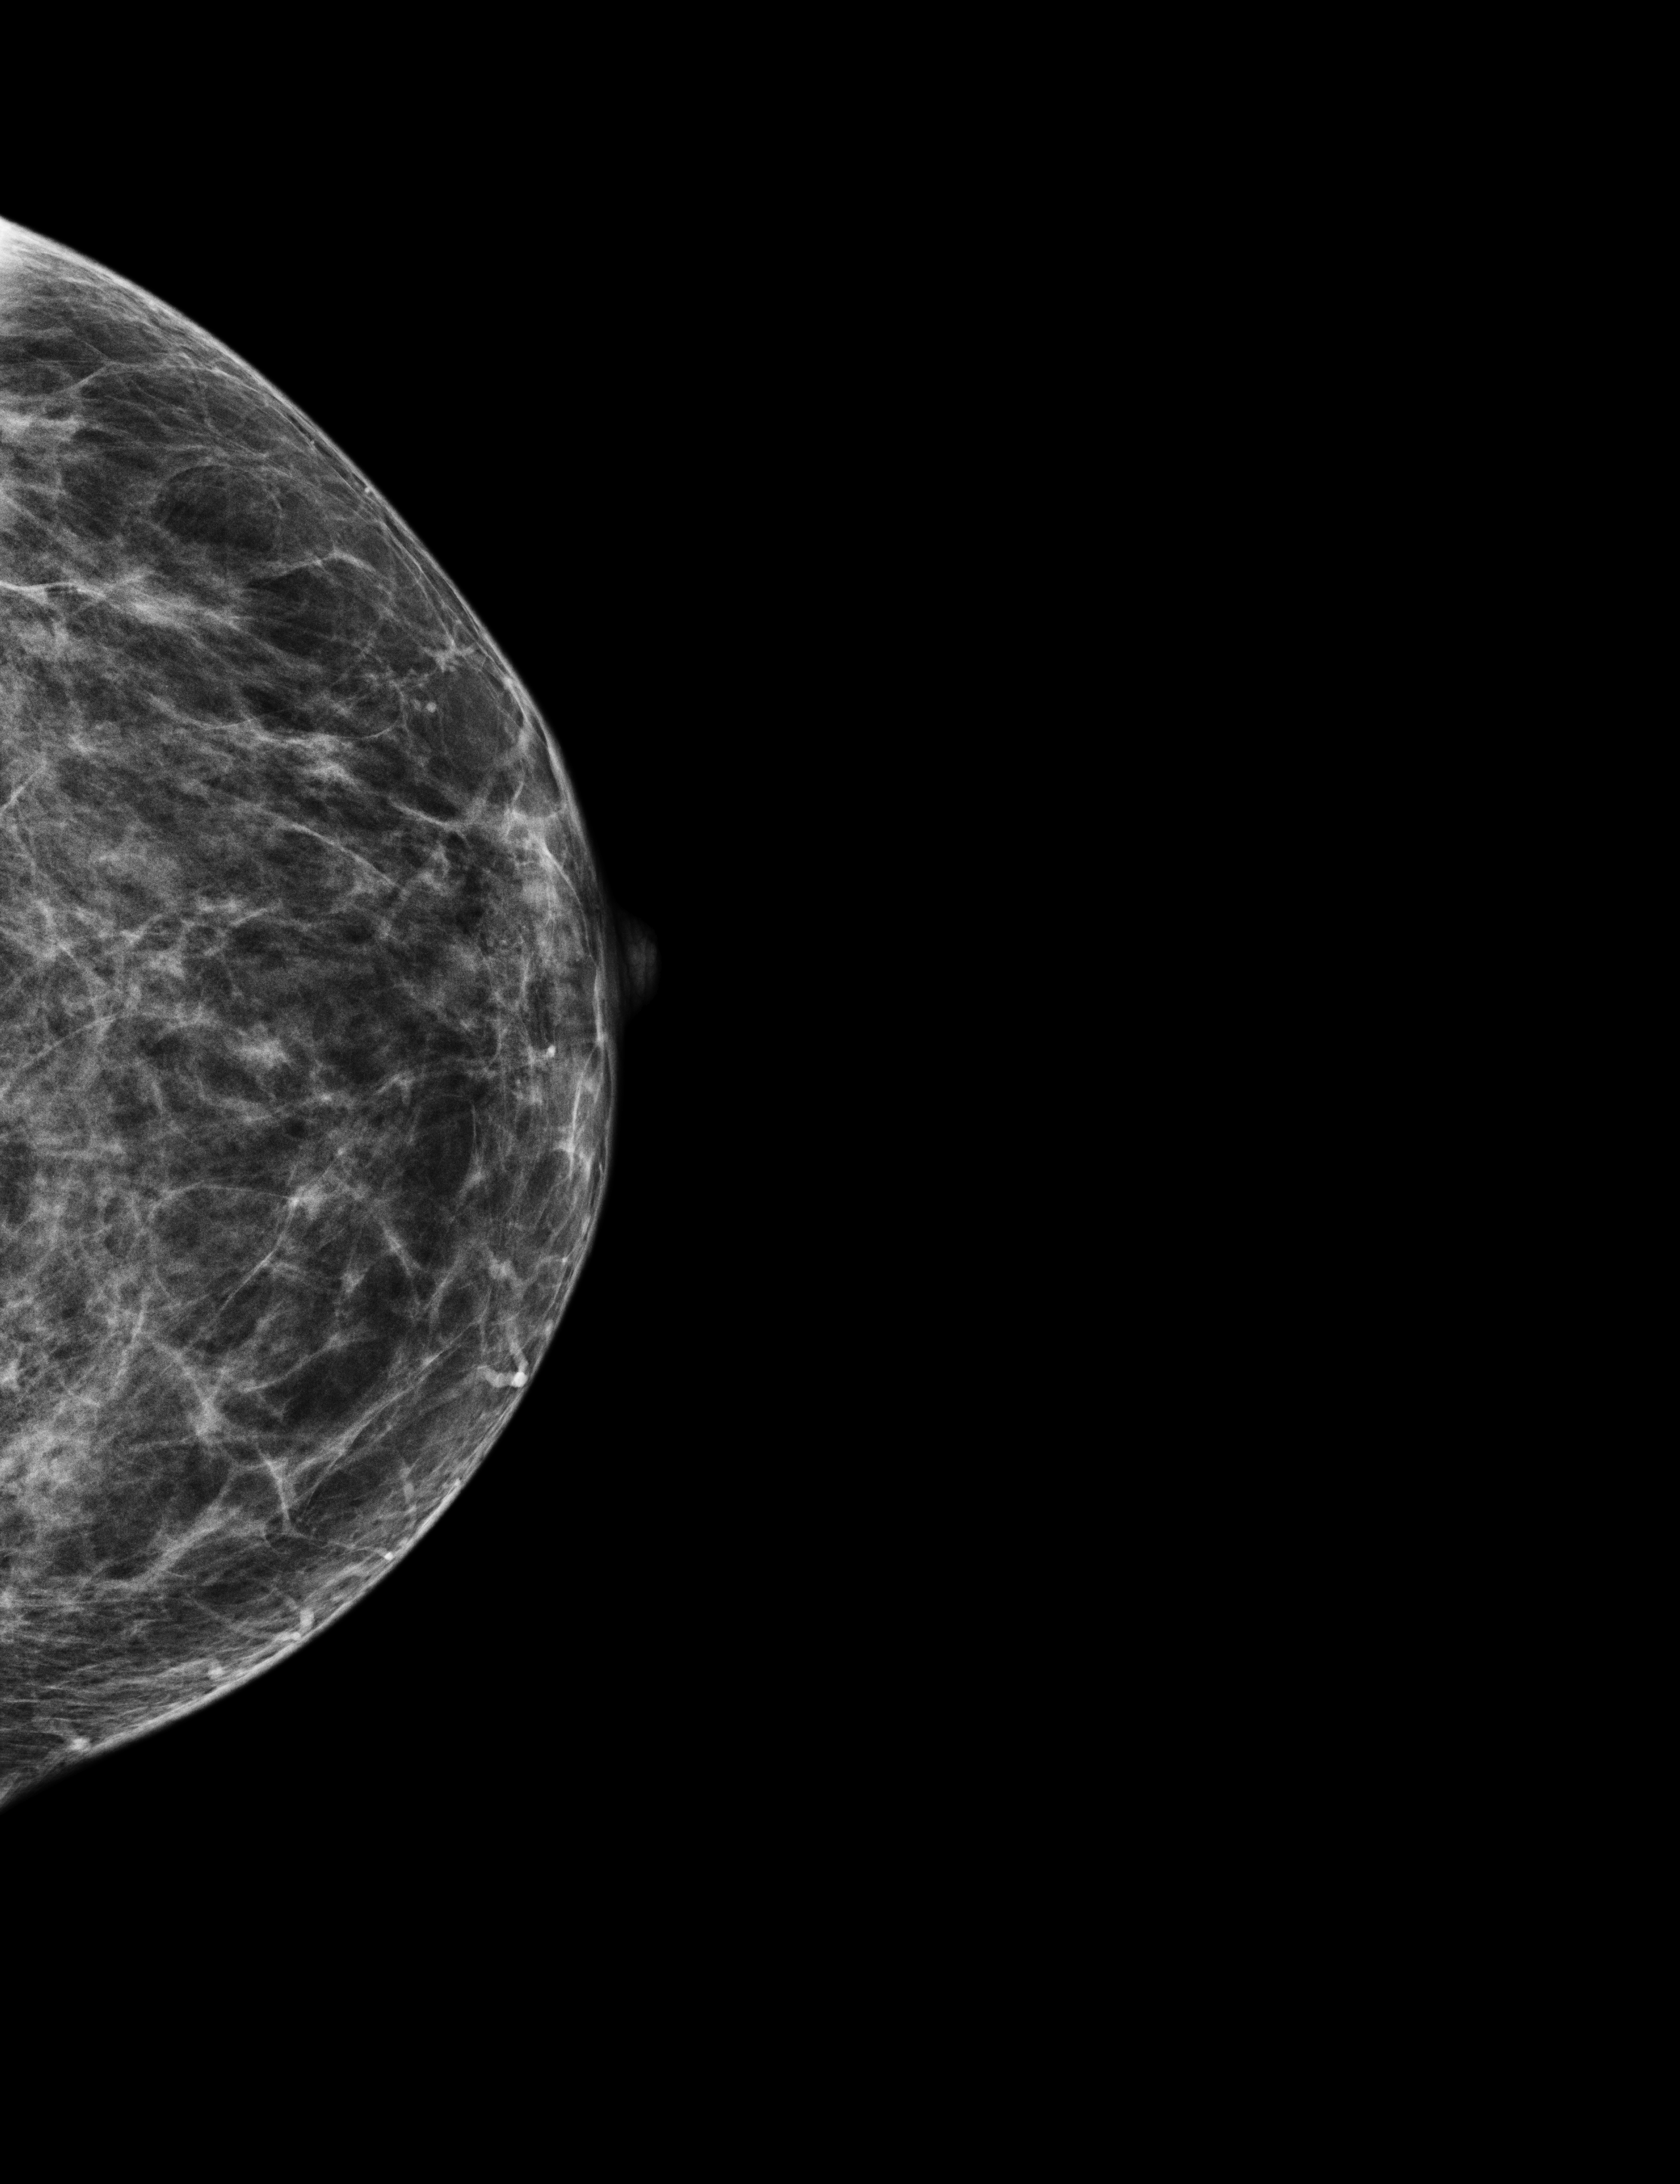
Annual screening mammography examination, compressed breast thickness 44 mm, system: Selenia Dimensions. Female patient, age 65 years.
Image type: full-field digital mammogram. Breast: left. Projection: cranio-caudal projection.